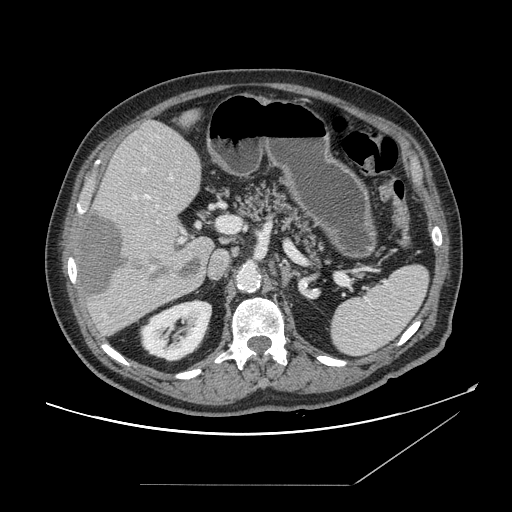
Contrast-enhanced abdominal CT, one axial slice. Soft-tissue window (W 400 / L 40 HU). 2.5 mm slice thickness. 512 × 512 image matrix, field of view 416 × 416 mm. Male patient, age 80 years. From the clinical record (not read from this slice): diagnosis: colorectal cancer liver metastases, imaged before liver resection; multiple liver metastases: no; largest metastasis: 2.2 cm; disease in both lobes: no.
Outlined on this slice (manually delineated by an expert):
- hepatic veins: bounding box [x1, y1, x2, y2] px = [143, 169, 173, 270]
- liver: [78, 110, 213, 336]
- planned liver remnant (the part of the liver to remain after resection): [98, 110, 213, 249]
- portal vein (with intrahepatic branches): [134, 196, 231, 243]
- liver metastasis: [85, 214, 202, 299]